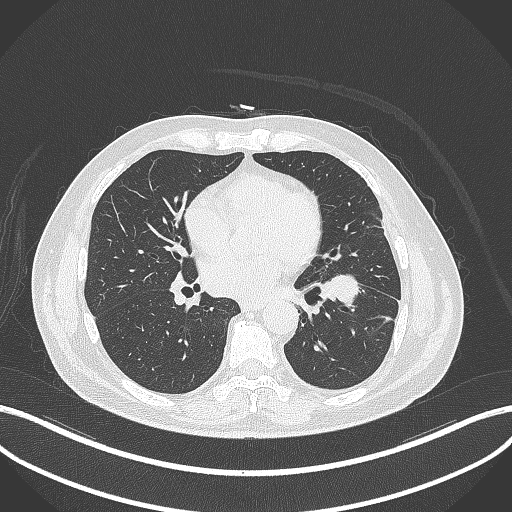
Chest CT, one axial slice; slice 167 of 230 in the series (ordered by position); 120 kVp; lung window (W 1500 / L -600 HU); 512 × 512 image matrix, field of view 400 × 400 mm. Patient: male, 68 years. From the clinical record (not read from this slice): clinical TNM (as recorded): T2b N0 M0.
Annotated regions visible in this slice (rectangle marked by the reading radiologist):
- lung tumour (recorded histology: squamous cell carcinoma): box from (x=321, y=268) to (x=365, y=311) px